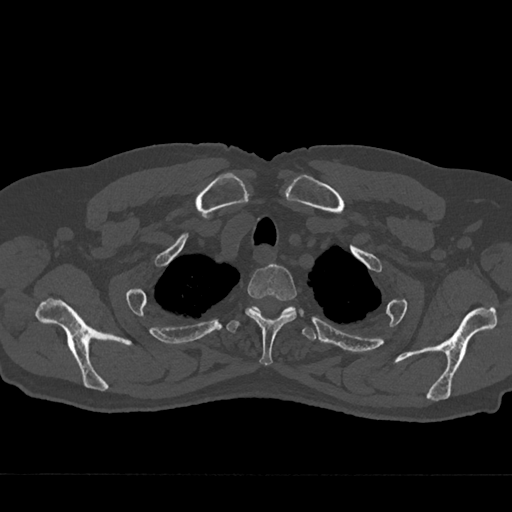
CT including the spine, one axial slice. Position 601 of 797 along the scan axis. Reconstruction kernel Br40s/3. Bone window (W 1800 / L 400 HU). 512 × 512 image matrix. Male patient, age 75 years. Case-level facts recorded for this patient, not image findings: primary cancer: renal; vertebrae with lytic lesions (as recorded): T4.
Annotated regions visible in this slice (semi-automatic segmentation, software-assisted and operator-edited):
- T2 vertebra: bounding box [x1, y1, x2, y2] px = [245, 264, 297, 365]
- T3 vertebra: [227, 306, 317, 340]